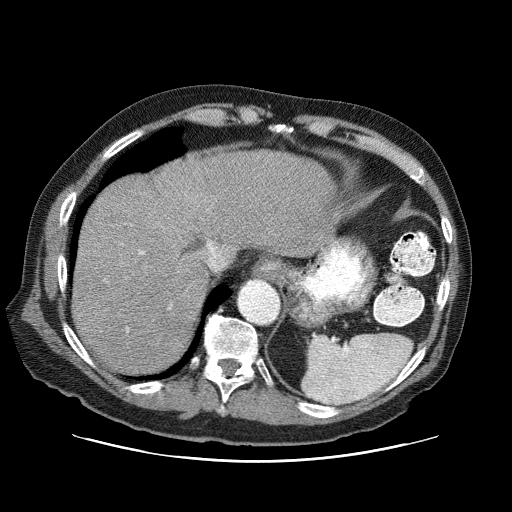
Contrast-enhanced abdominal CT (liver protocol), one axial slice; slice 61 of 87 in the series (ordered by position); one of 3 acquisitions stored at this slice position; soft-tissue window (W 400 / L 40 HU); 512 × 512 image matrix, field of view 400 × 400 mm. Case-level facts recorded for this patient, not image findings: diagnosis: hepatocellular carcinoma (patient treated with transarterial chemoembolisation; whether this scan precedes or follows treatment is not stated here); TNM stage (as recorded): Stage-IIIA; Child-Pugh class: A; tumour differentiation: well differentiated; tumour nodularity: multinodular.
Outlined on this slice (semi-automatic segmentation, software-assisted and operator-edited):
- liver parenchyma outside the tumour (the mass and vessels are separate outlines, so this box may not span the whole liver): bounding box [x1, y1, x2, y2] px = [72, 150, 340, 374]
- liver vessels: [127, 243, 211, 332]